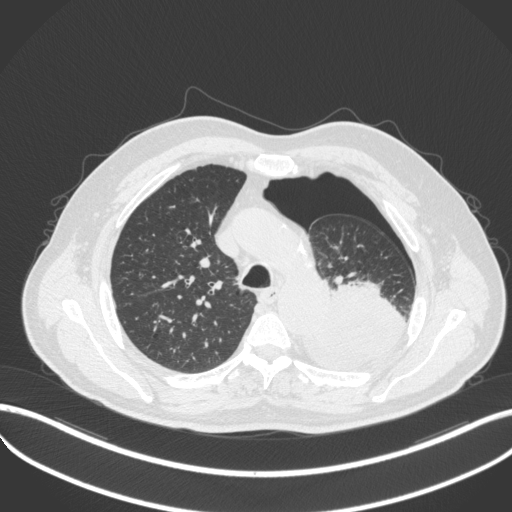
Chest CT, one axial slice. Position 373 of 466 along the scan axis. Reconstruction kernel B31f. 120 kVp. Lung window (W 1500 / L -600 HU). 512 × 512 image matrix, field of view 400 × 400 mm. Male patient, age 76 years. Case-level facts recorded for this patient, not image findings: clinical TNM (as recorded): T3 N0 M1b.
Annotated regions visible in this slice (rectangle marked by the reading radiologist):
- lung tumour (recorded histology: adenocarcinoma): box from (x=302, y=271) to (x=412, y=374) px